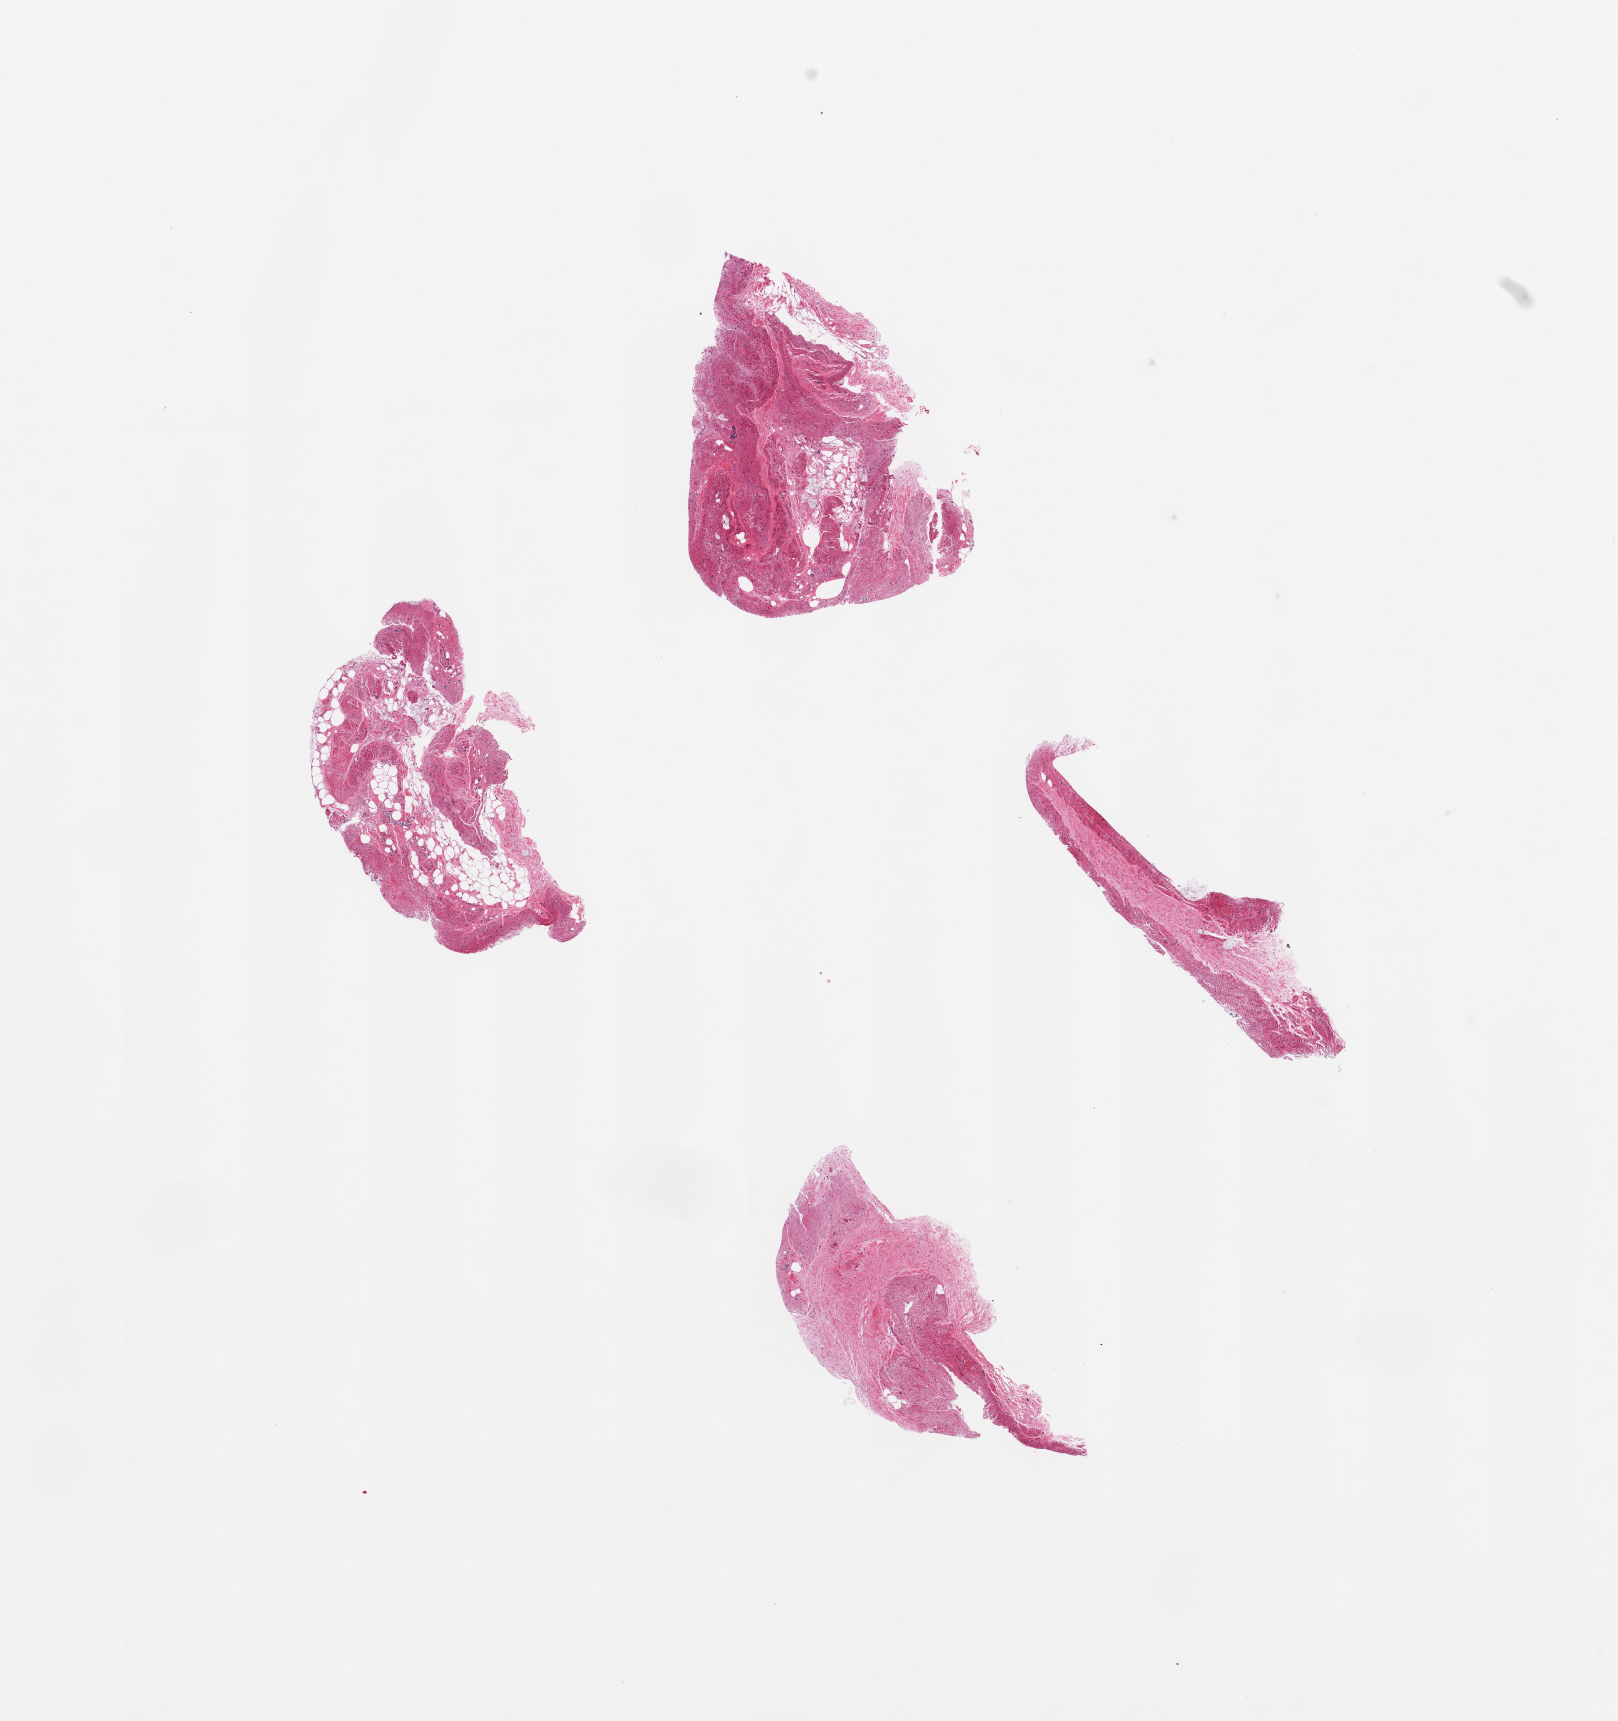
Hematoxylin and eosin (H&E) whole-slide image, brightfield — whole scanned area (about 12.8 x 13.6 mm) shown as a low-resolution overview, PAXgene-fixed, paraffin-embedded tissue, target tissue: sigmoid colon, tissue donor sample. Donor: female.
Review note (as recorded): 4 pieces, trace muscularis, mainlly serosal fat/ connective tissue.